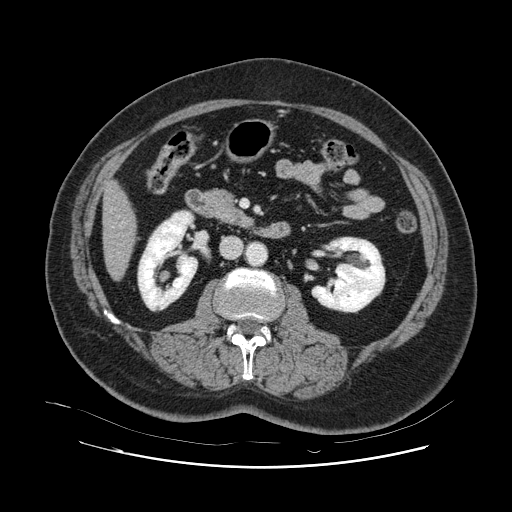
Contrast-enhanced abdominal CT, one axial slice; slice 27 of 132 in the series (ordered by position); 120 kVp; intravenous contrast given; soft-tissue window (W 400 / L 40 HU); 2.5 mm slice thickness; 512 × 512 image matrix, field of view 391 × 391 mm. Female patient, age 73 years. Case-level facts recorded for this patient, not image findings: diagnosis: colorectal cancer liver metastases, imaged before liver resection; multiple liver metastases: no; largest metastasis: 7 cm.
Structures marked on this image (outlined manually by an expert reader):
- liver: bounding box <104,185,134,278> (left, top, right, bottom; pixels)
- planned liver remnant (the part of the liver to remain after resection): <104,185,135,278>